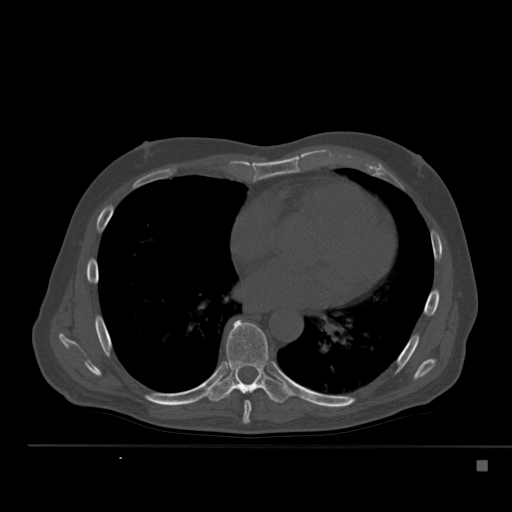
CT including the spine, one axial slice; slice 313 of 517 in the series (ordered by position); bone window (W 1800 / L 400 HU); 1.5 mm slice thickness; 512 × 512 image matrix, field of view 408 × 408 mm. Male patient, age 70 years. From the clinical record (not read from this slice): primary cancer: renal.
Outlined on this slice (semi-automatic segmentation, software-assisted and operator-edited):
- T7 vertebra: box from (x=242, y=401) to (x=251, y=424) px
- T8 vertebra: (x=206, y=320)–(x=290, y=403)